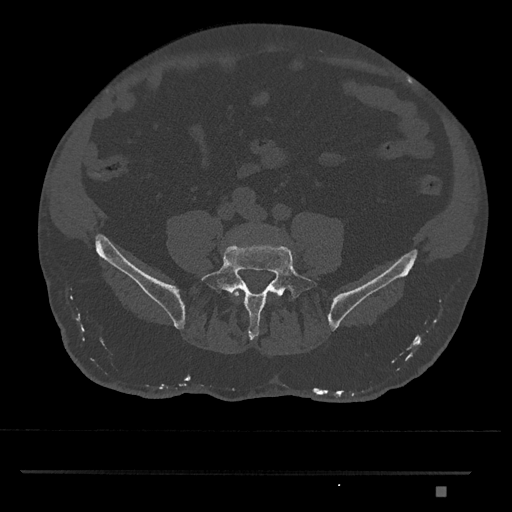
CT including the spine, one axial slice; slice 565 of 1134 in the series (ordered by position); reconstruction kernel Br40s/3; bone window (W 1800 / L 400 HU); 0.5 mm slice thickness; 512 × 512 image matrix, field of view 429 × 429 mm. Male patient, age 65 years. Case-level facts recorded for this patient, not image findings: primary cancer: prostate.
Outlined on this slice (semi-automatically segmented with operator editing):
- L4 vertebra: bounding box [x1, y1, x2, y2] px = [231, 291, 279, 299]
- L5 vertebra: [201, 244, 318, 340]